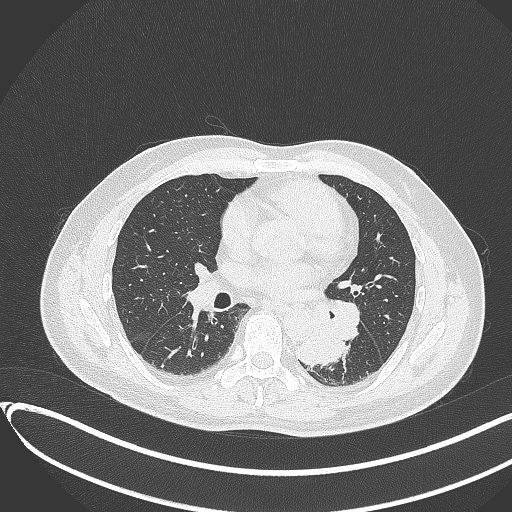
Chest CT, one axial slice. Position 172 of 417 along the scan axis. Lung window (W 1500 / L -600 HU). 512 × 512 image matrix, field of view 400 × 400 mm. Patient: male, 54 years. From the clinical record (not read from this slice): clinical TNM (as recorded): T3 N0 M0.
Outlined on this slice (bounding box drawn by a radiologist):
- lung tumour (recorded histology: squamous cell carcinoma): bounding box <298,320,351,366> (left, top, right, bottom; pixels)